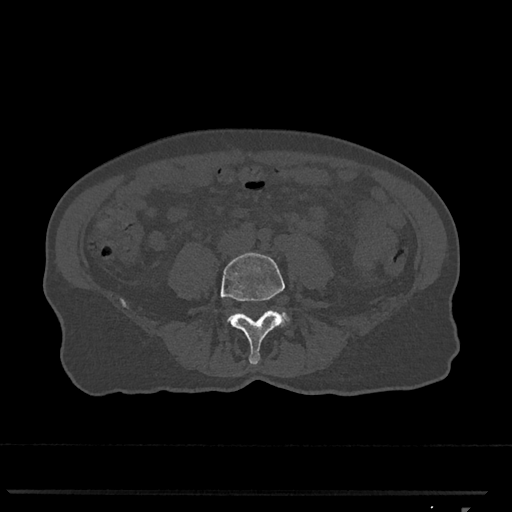
CT including the spine, one axial slice; position 200 of 793 along the scan axis; reconstruction kernel Br40s/3; bone window (W 1800 / L 400 HU); 0.5 mm slice thickness; 512 × 512 image matrix. Female patient, age 62 years. From the clinical record (not read from this slice): primary cancer: renal.
Structures marked on this image (semi-automatically segmented with operator editing):
- L4 vertebra: bounding box (x1, y1, x2, y2) in pixels: (220, 253, 285, 365)
- L5 vertebra: (227, 312, 290, 323)